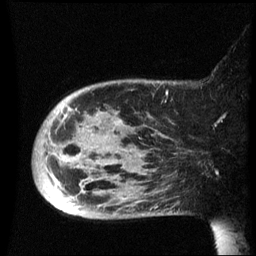
Breast MRI (dynamic contrast-enhanced), one sagittal slice; slice 14 of 60 in the series (ordered by position); dynamic contrast-enhanced series, image 2 of 3 at this slice position (ordered by acquisition); 1.5 T; TE 4.2 ms, TR 8.4 ms; 2.5 mm slice thickness; 256 × 256 image matrix. Patient: female, 49 years.
Annotated regions visible in this slice (semi-automatic segmentation, software-assisted and operator-edited):
- analysis volume of interest (the breast-tissue region the enhancement analysis was run in; not a lesion): box from (x=33, y=80) to (x=184, y=219) px
- tumour enhancement mask (voxels above the 70 % enhancement threshold inside the analysis volume of interest): (x=53, y=108)–(x=73, y=185)